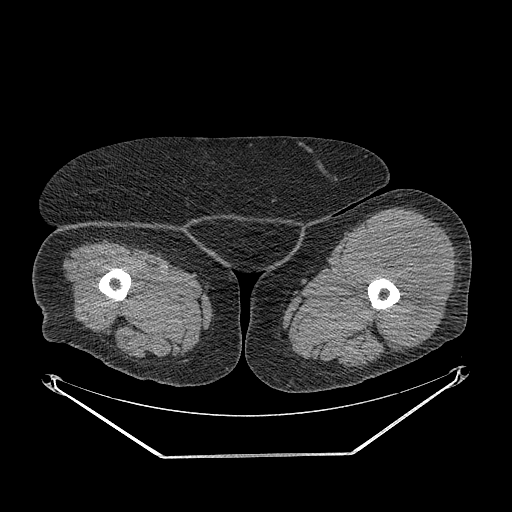
CT of an extremity soft-tissue mass (from a PET/CT study), one axial slice. Position 240 of 267 along the scan axis. Reconstruction kernel STANDARD. Soft-tissue window (W 400 / L 40 HU). 512 × 512 image matrix. Female patient. Case-level facts recorded for this patient, not image findings: histological type: undifferentiated – high grade; grade: high; site of the primary tumour: left thigh.
Structures marked on this image (expert contour drawn on MRI and transferred to this co-registered scan by the dataset authors):
- gross tumour volume including surrounding oedema: bounding box <352,226,442,350> (left, top, right, bottom; pixels)
- gross tumour volume (mass): <352,226,442,350>